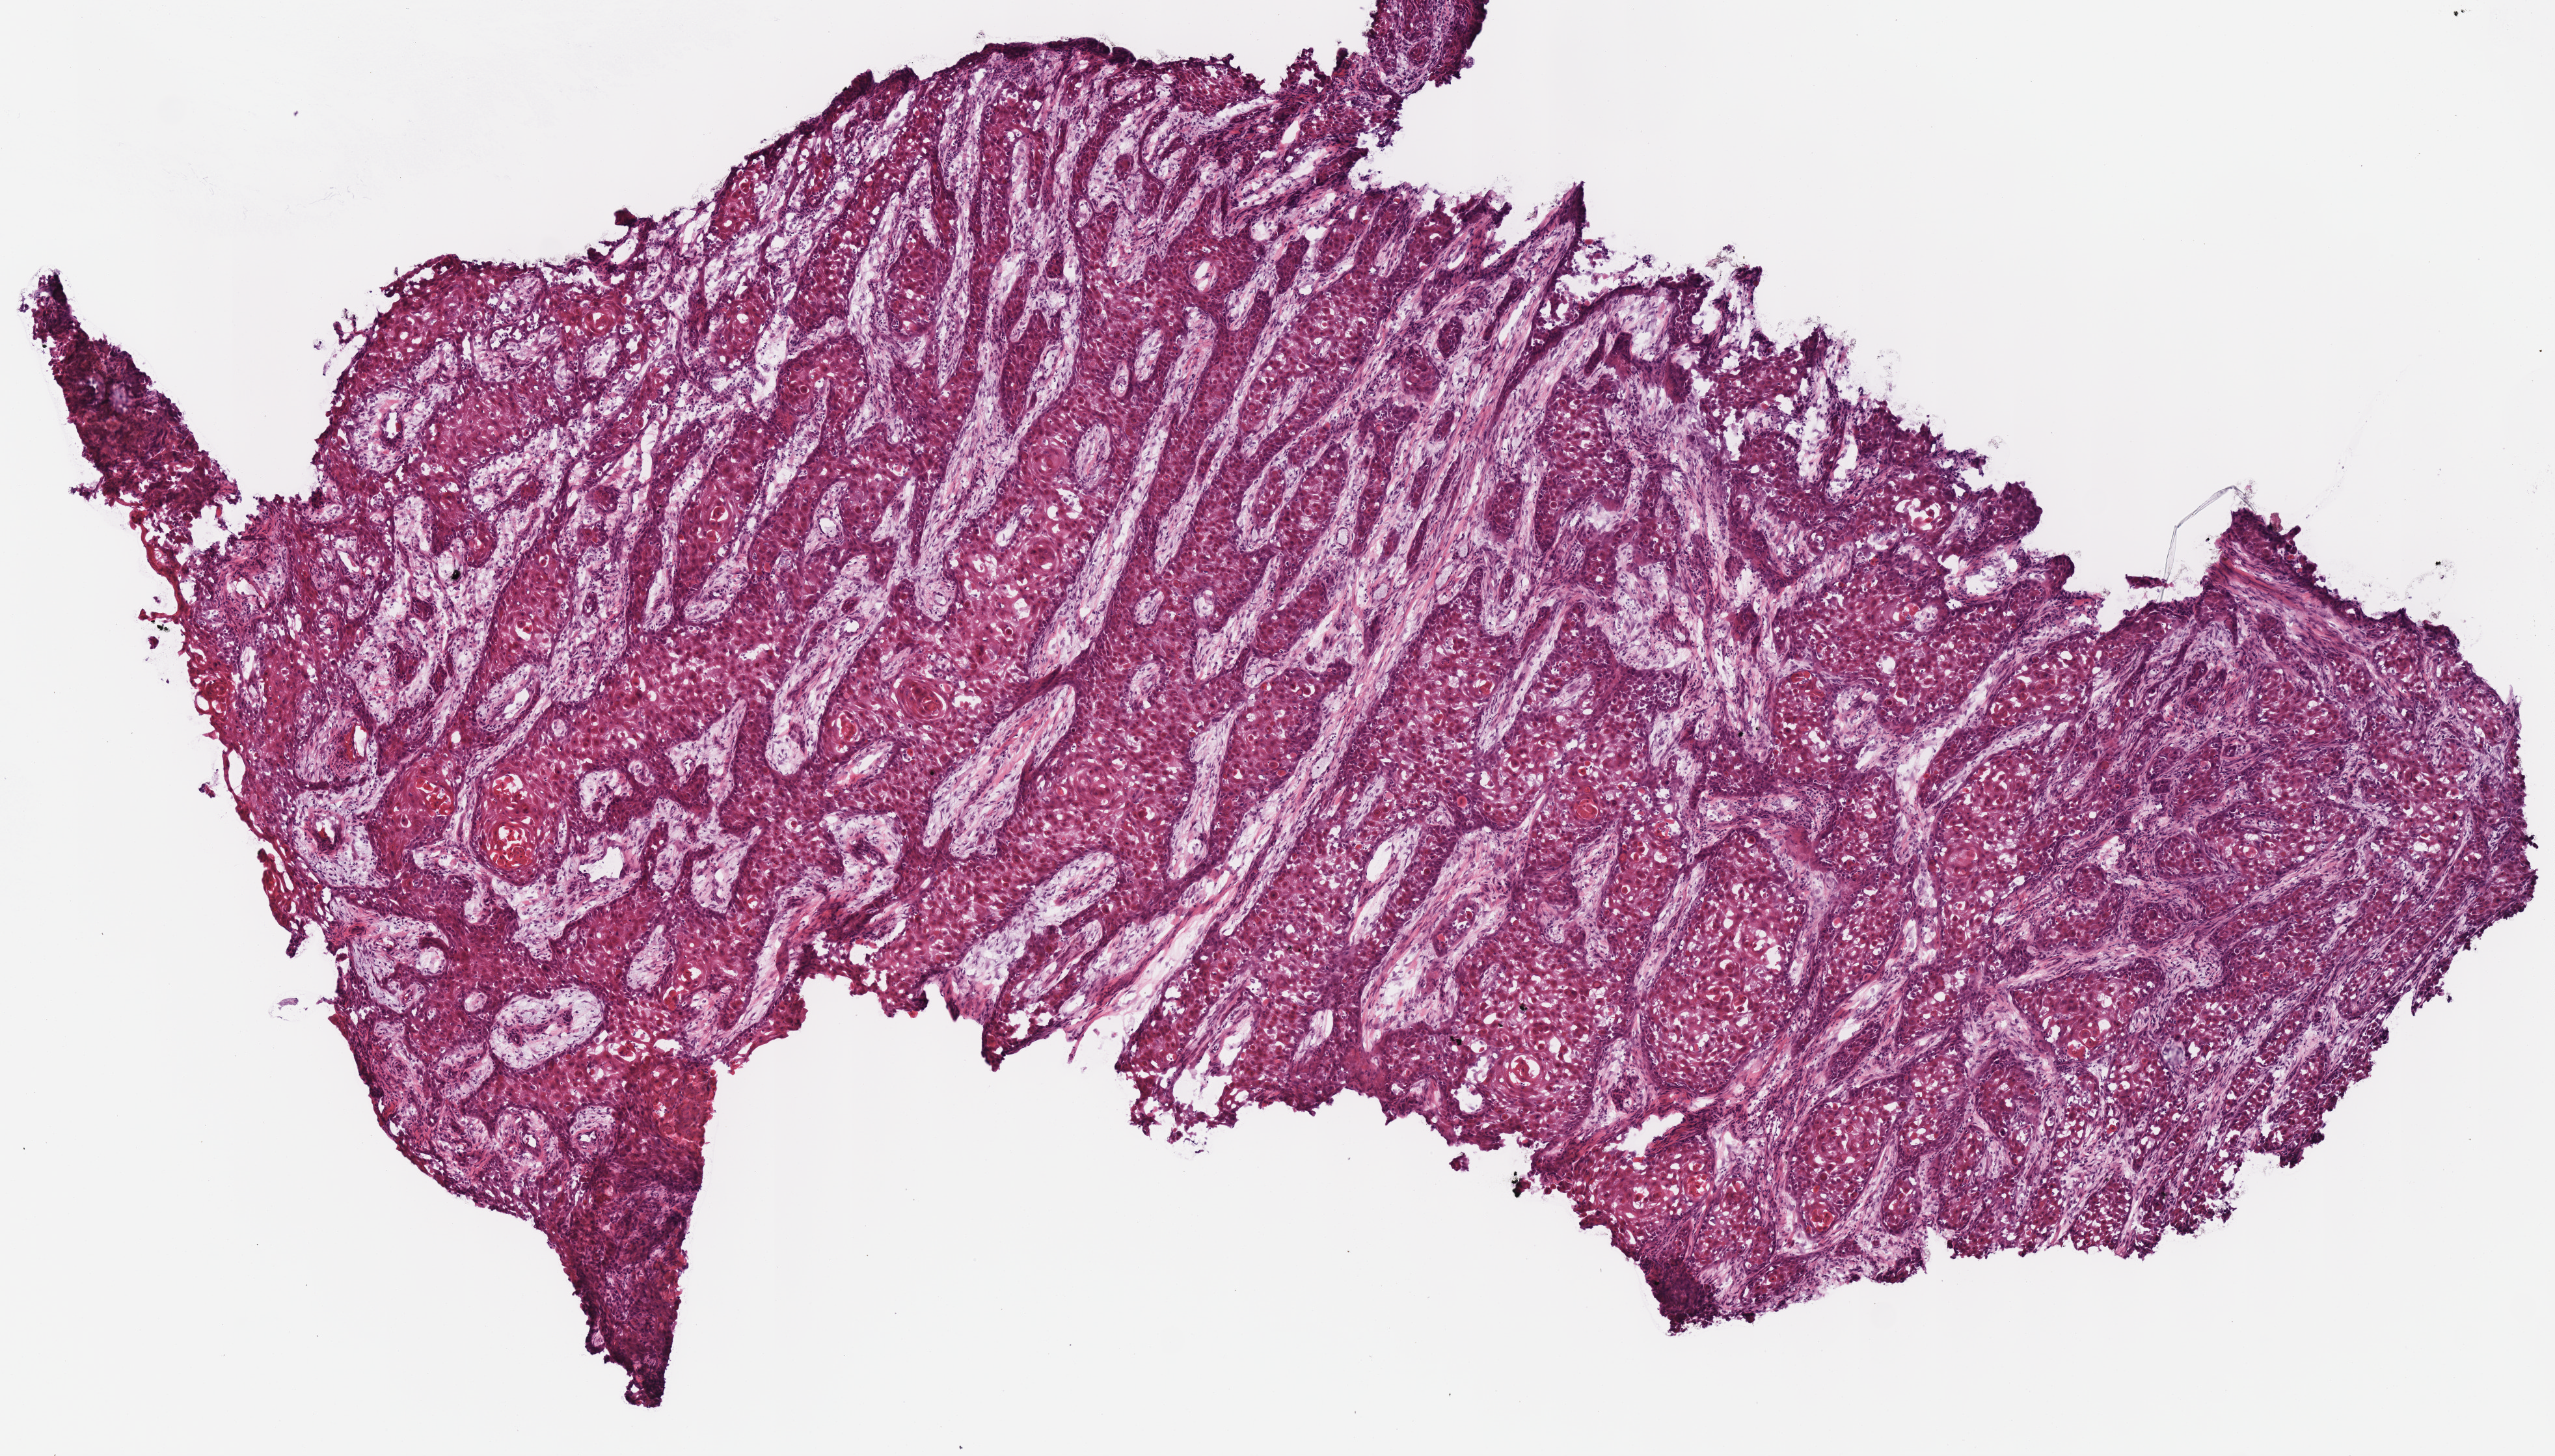
H&E whole-slide image, shown as a low-resolution overview of the whole scanned area (about 7.7 x 4.4 mm). Frozen section from the top of the tissue portion. Head and neck, primary tumour sample. Male, age 64 years at initial diagnosis. Histologic grade: G2 (moderately differentiated). Slide review estimates, as recorded: tumour cells 88%, tumour nuclei 85%, normal cells 0%, stromal cells 12%, necrosis 0%.
AJCC pathologic stage: IVA (7th edition). Histologic diagnosis: Squamous cell carcinoma, NOS (overlapping lesion of lip, oral cavity and pharynx). Laterality: left. TNM: T4a N1.